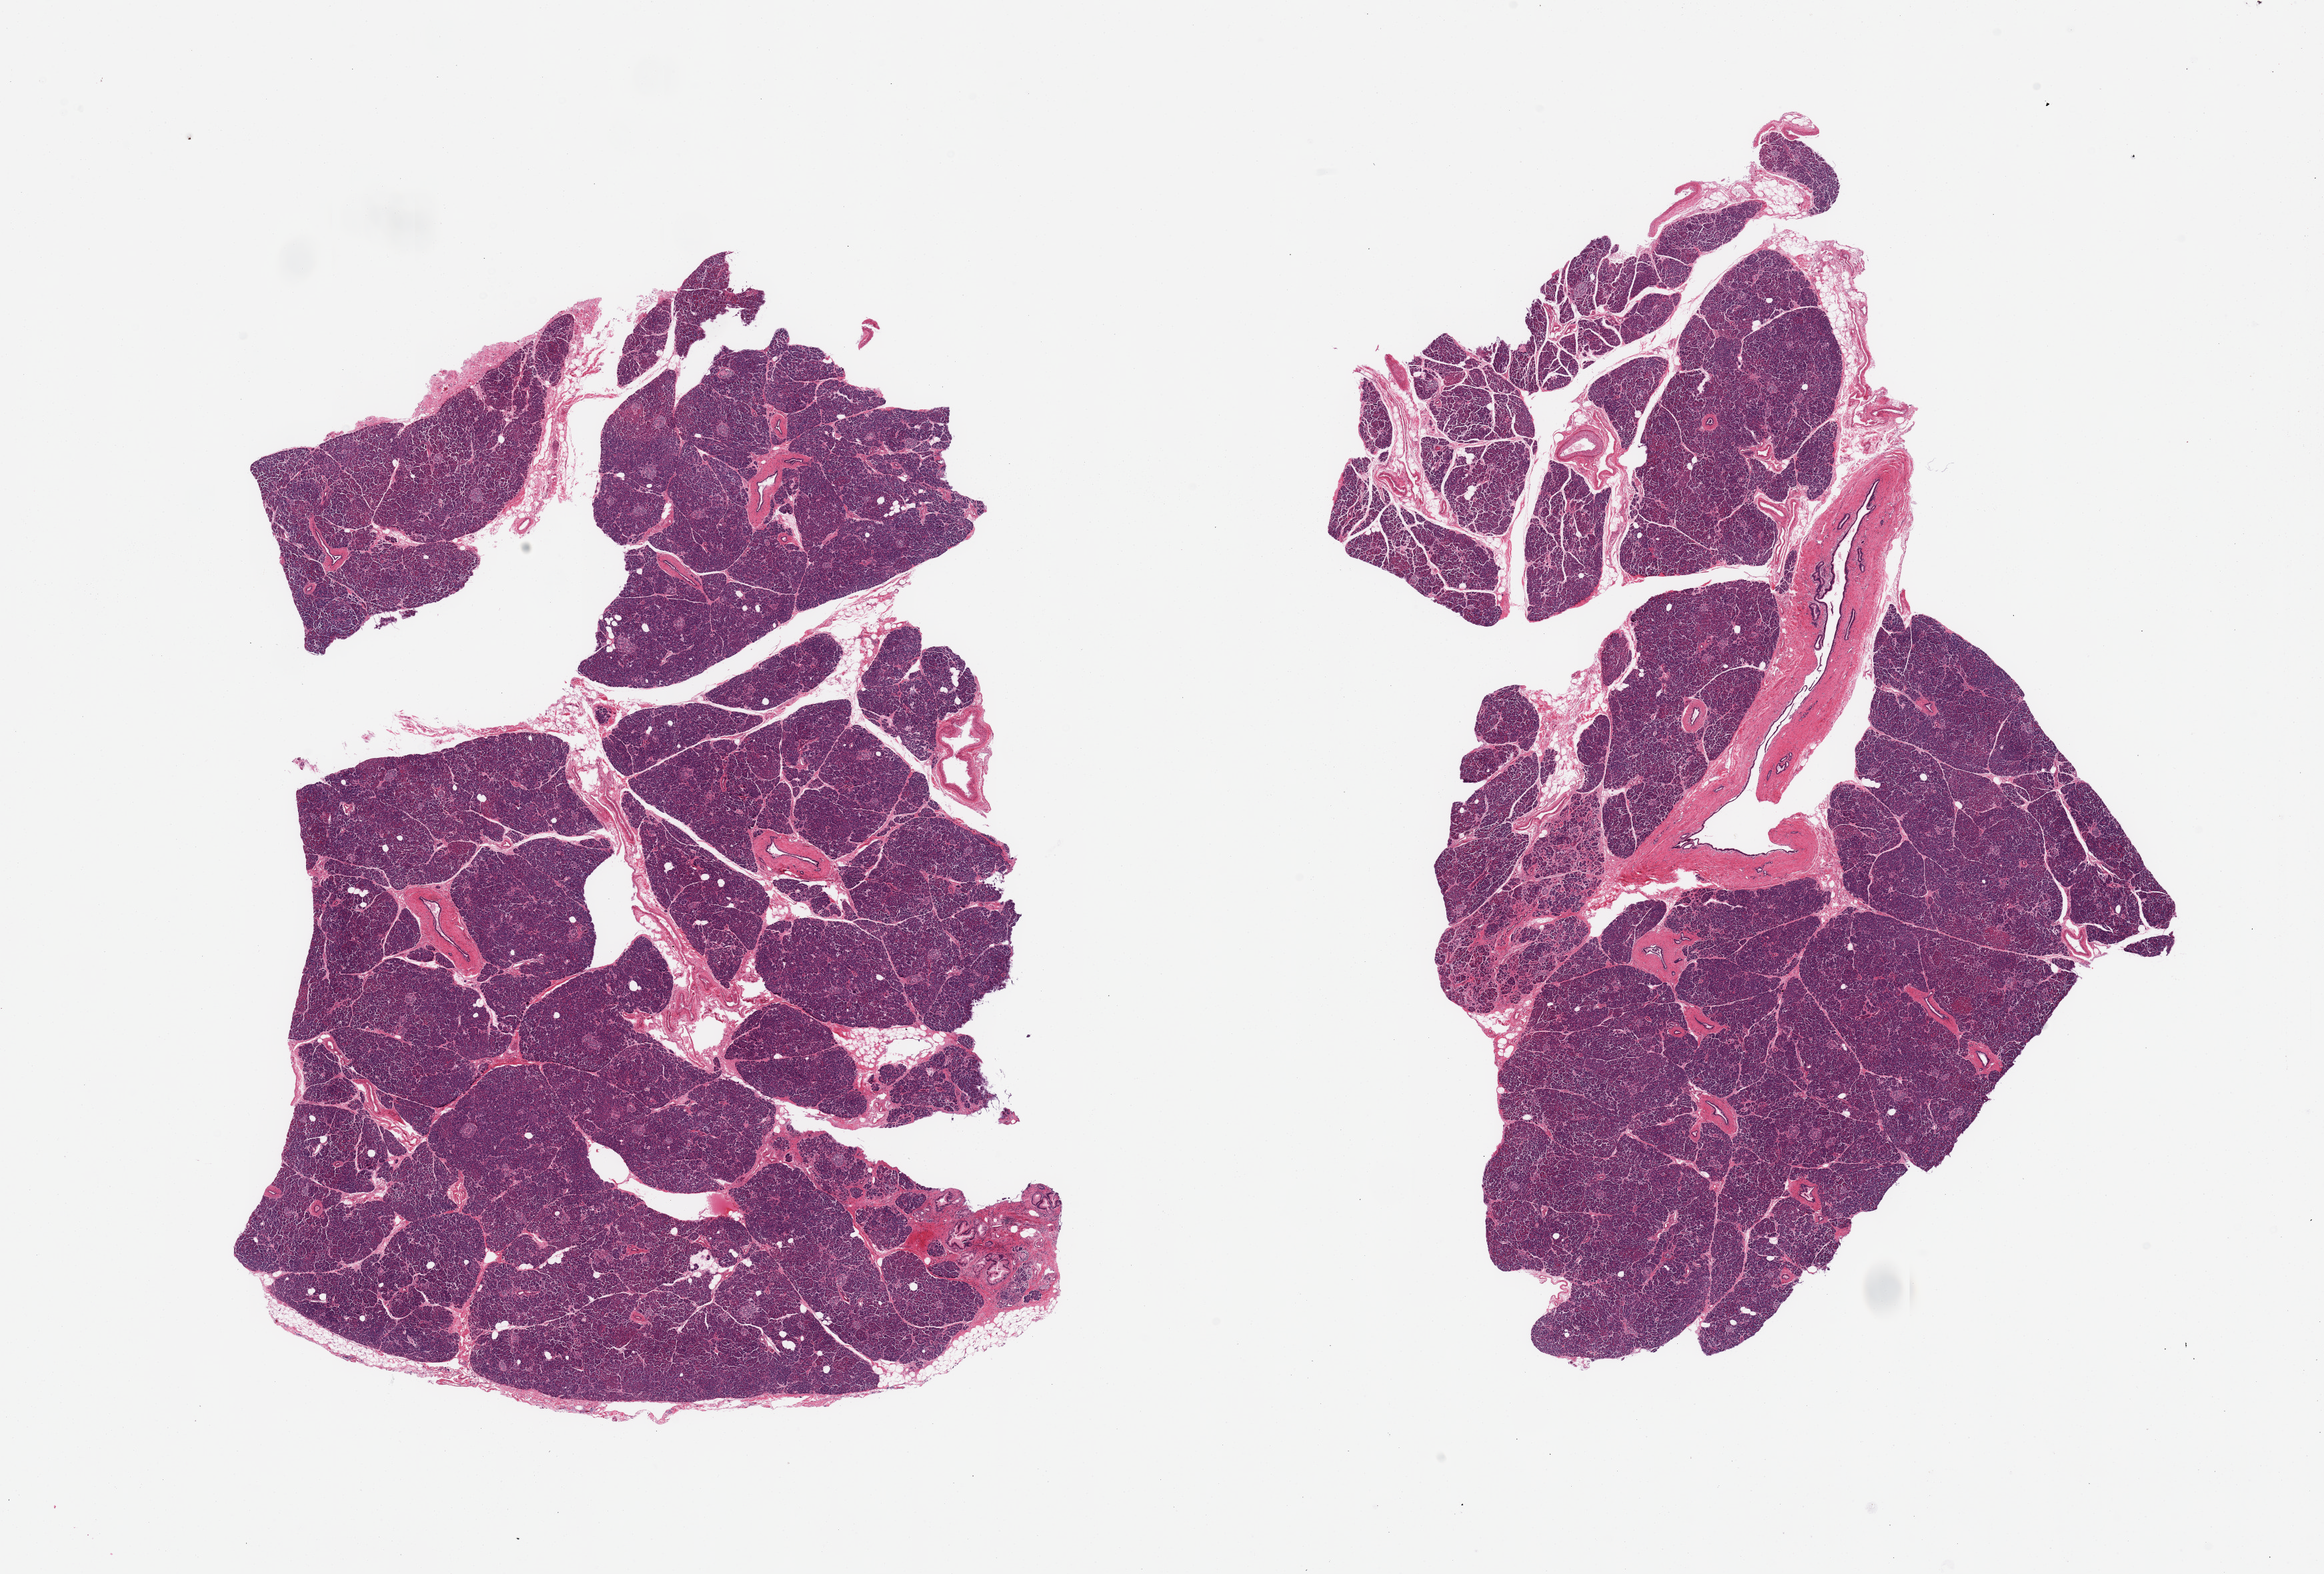
H&E whole-slide image — low-resolution overview of the scanned area, about 27.6 x 18.7 mm (slide scanned at 20x); PAXgene-fixed paraffin-embedded (PFPE) section; section of pancreas (target tissue); tissue donor sample. Donor: male.
Reviewer comment on this tissue sample: 2 pieces; preserved parenchyma with Langerhans islets; moderately autolyzed septal fat; larger ductal structure with fibrotic band.